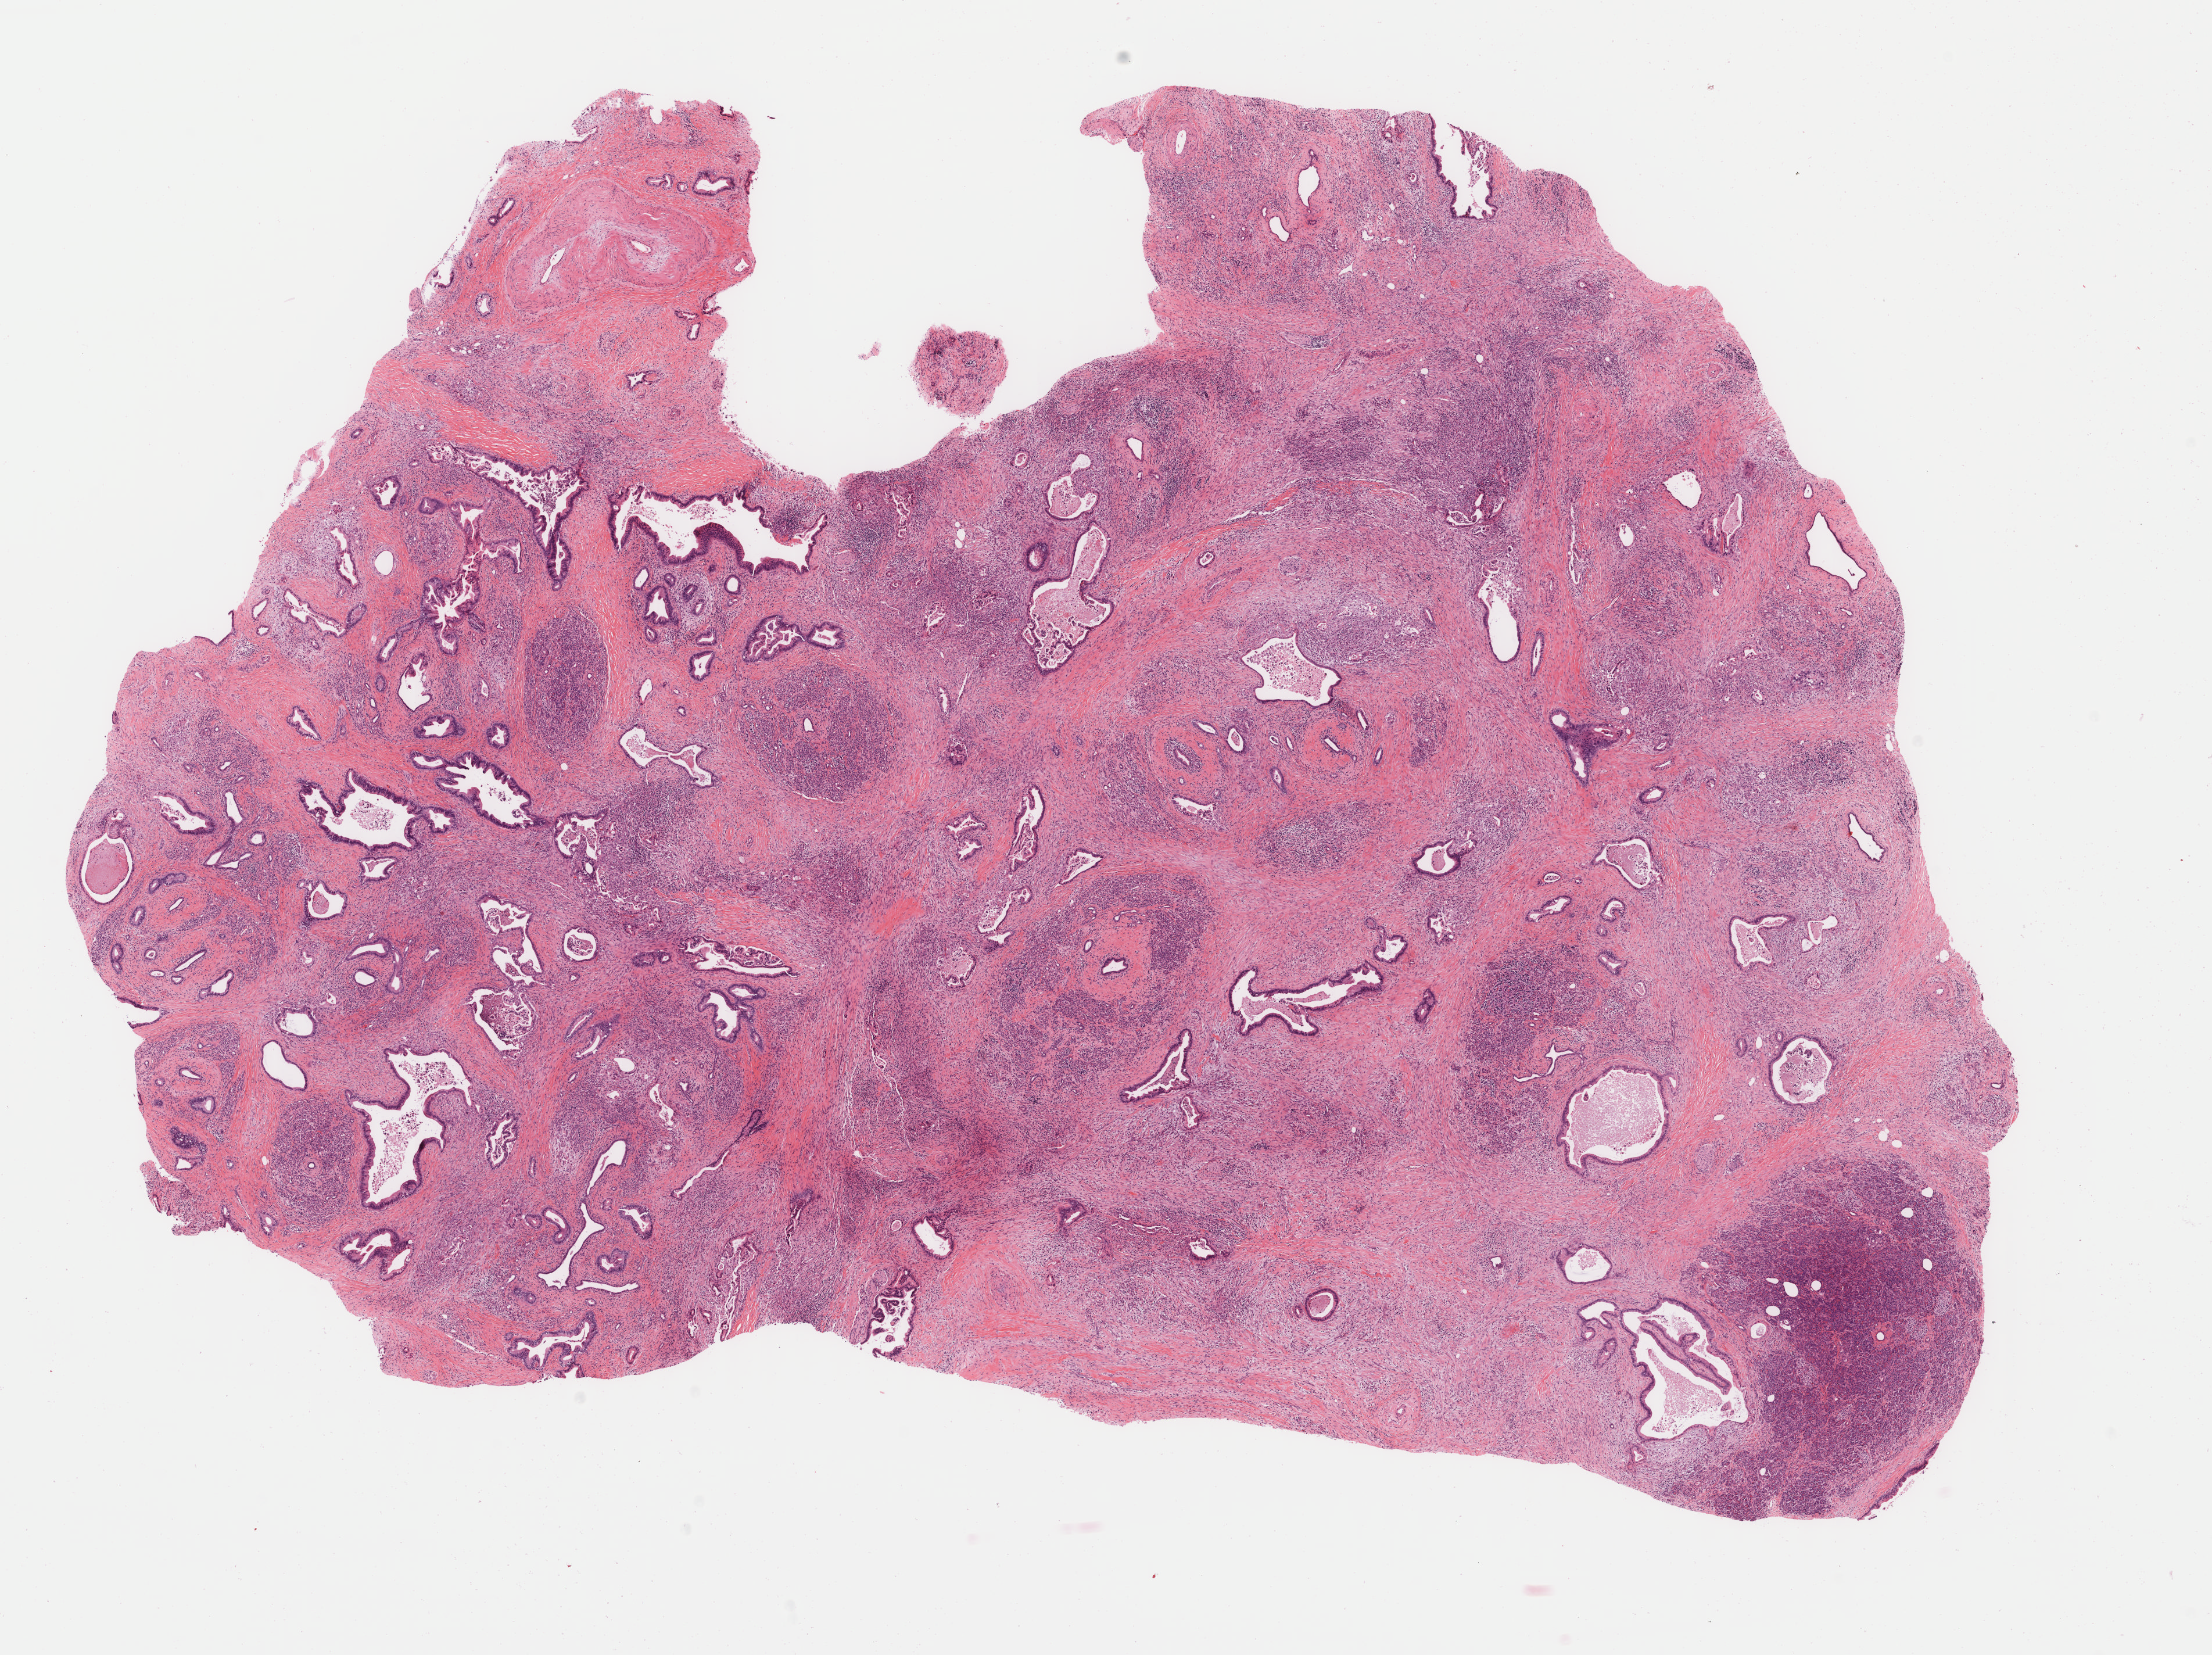
Whole-slide histology image, H&E, shown as a low-resolution overview of the whole scanned area (about 15.1 x 11.3 mm, from a 40x scan); formalin-fixed paraffin-embedded (FFPE) diagnostic section; sample: primary tumour, pancreas. Female patient; age at initial diagnosis 71 years.
Diagnosis: Infiltrating duct carcinoma, NOS (head of pancreas).